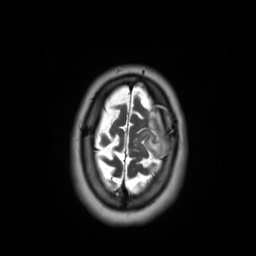
Brain MRI from a brain-tumour surgery series, one axial slice. Position 49 of 59 along the scan axis. 256 × 256 image matrix, field of view 250 × 250 mm. Case-level facts recorded for this patient, not image findings: histopathology: Oligodendroglioma; WHO grade: 2; IDH mutation: yes.
Annotated regions visible in this slice (outlined manually by an expert reader):
- tumour: bounding box [x1, y1, x2, y2] px = [139, 122, 180, 158]